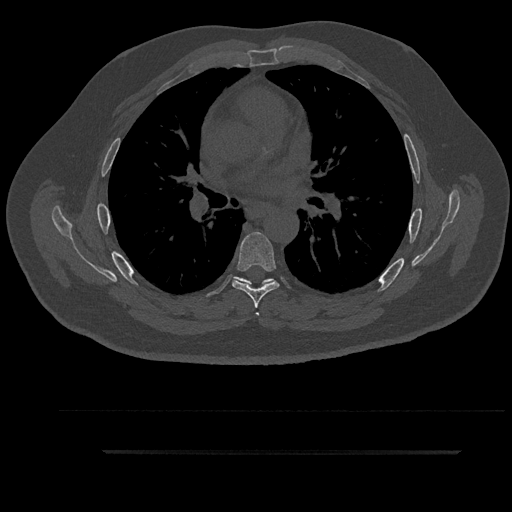
CT including the spine, one axial slice; slice 572 of 797 in the series (ordered by position); reconstruction kernel Br40s/3; bone window (W 1800 / L 400 HU); 0.5 mm slice thickness; 512 × 512 image matrix, field of view 432 × 432 mm. Male patient, age 63 years. From the clinical record (not read from this slice): primary cancer: renal; vertebrae with lytic lesions (as recorded): T8.
Outlined on this slice (semi-automatic segmentation, software-assisted and operator-edited):
- T5 vertebra: bounding box [x1, y1, x2, y2] px = [235, 277, 274, 316]
- T6 vertebra: [232, 232, 279, 308]
- T7 vertebra: [242, 278, 275, 286]